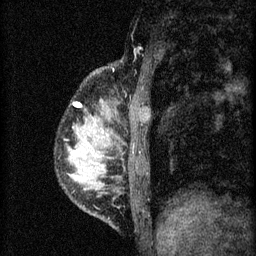
Breast MRI (dynamic contrast-enhanced), one sagittal slice; position 11 of 60 along the scan axis; 3 images stored at this slice position (order not interpretable as contrast timing); 1.5 T; TE 4.2 ms, TR 8.2 ms; 2 mm slice thickness; 256 × 256 image matrix. Patient: female, 37 years.
Outlined on this slice (semi-automatically segmented with operator editing):
- analysis volume of interest (the breast-tissue region the enhancement analysis was run in; not a lesion): bounding box [x1, y1, x2, y2] px = [66, 98, 140, 181]
- tumour enhancement mask (voxels above the 70 % enhancement threshold inside the analysis volume of interest): [74, 102, 80, 107]